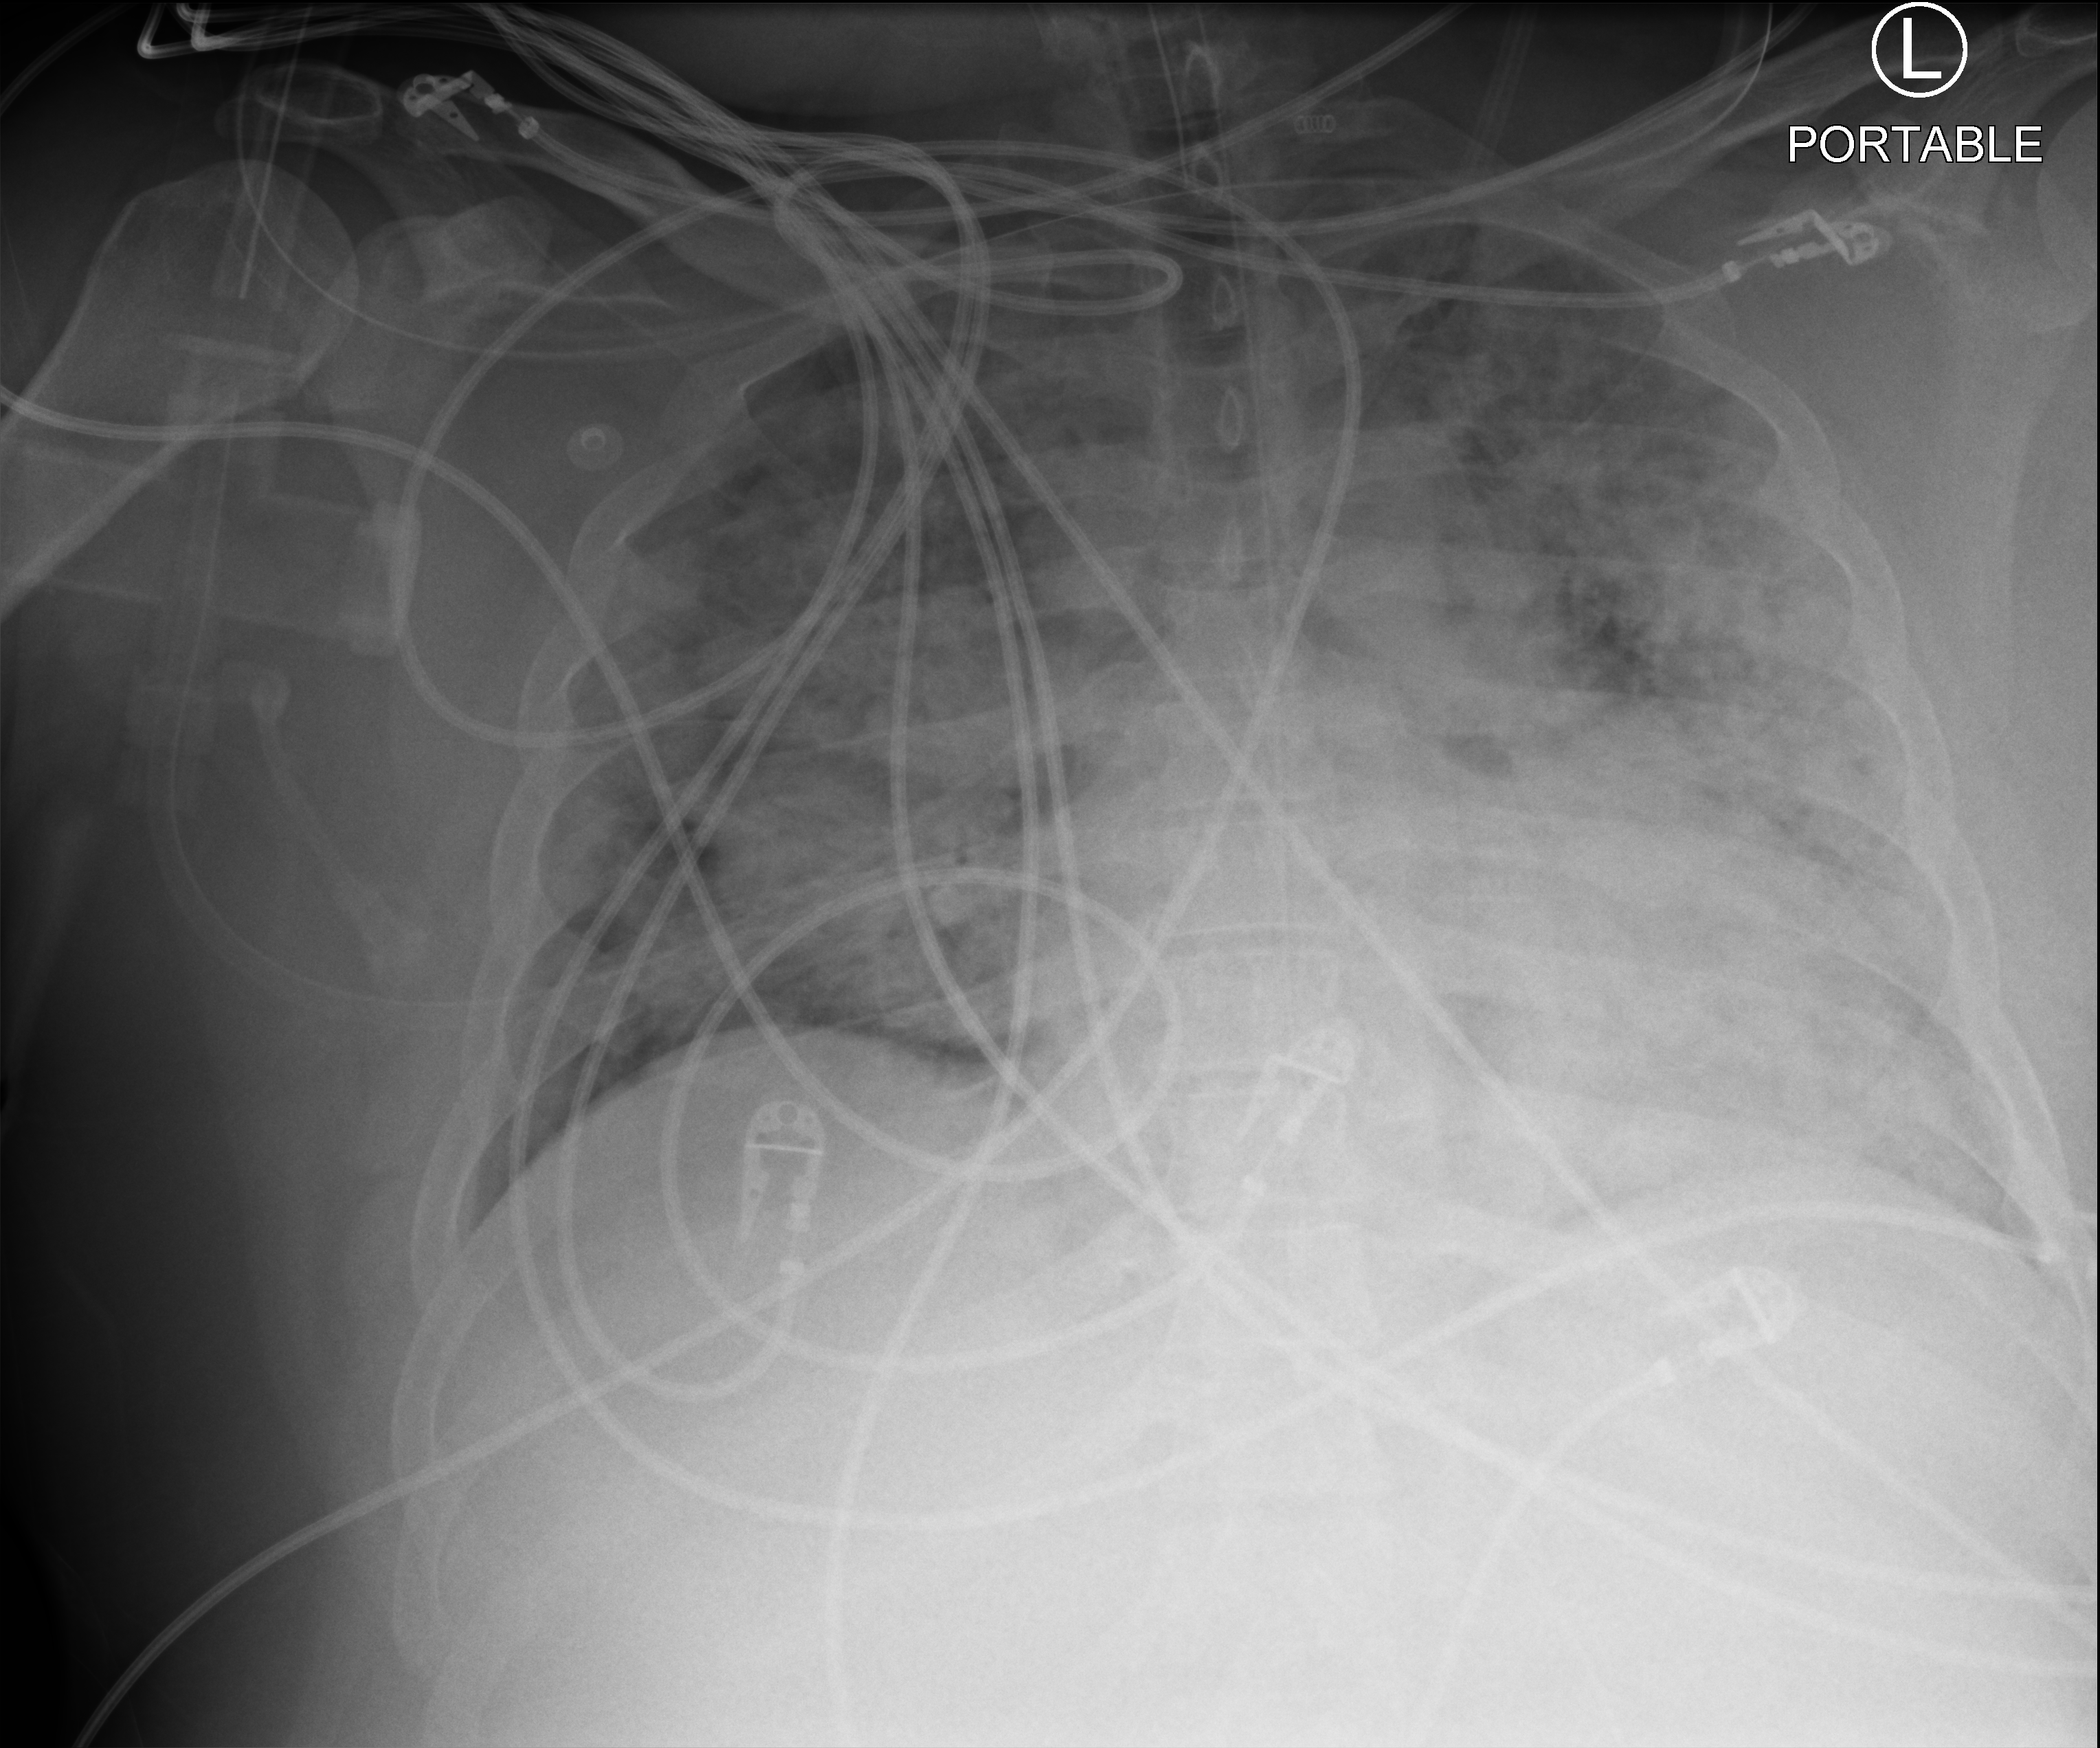
Portable chest radiograph; anteroposterior (AP) projection. Adult patient hospitalised with COVID-19, age 18–59 years.
Hospital-stay facts (about this admission, not read from this image; timing relative to this image not recorded): diabetes (admission record): no; mechanically ventilated during this hospital stay: yes; admitted to intensive care during this hospital stay: yes.